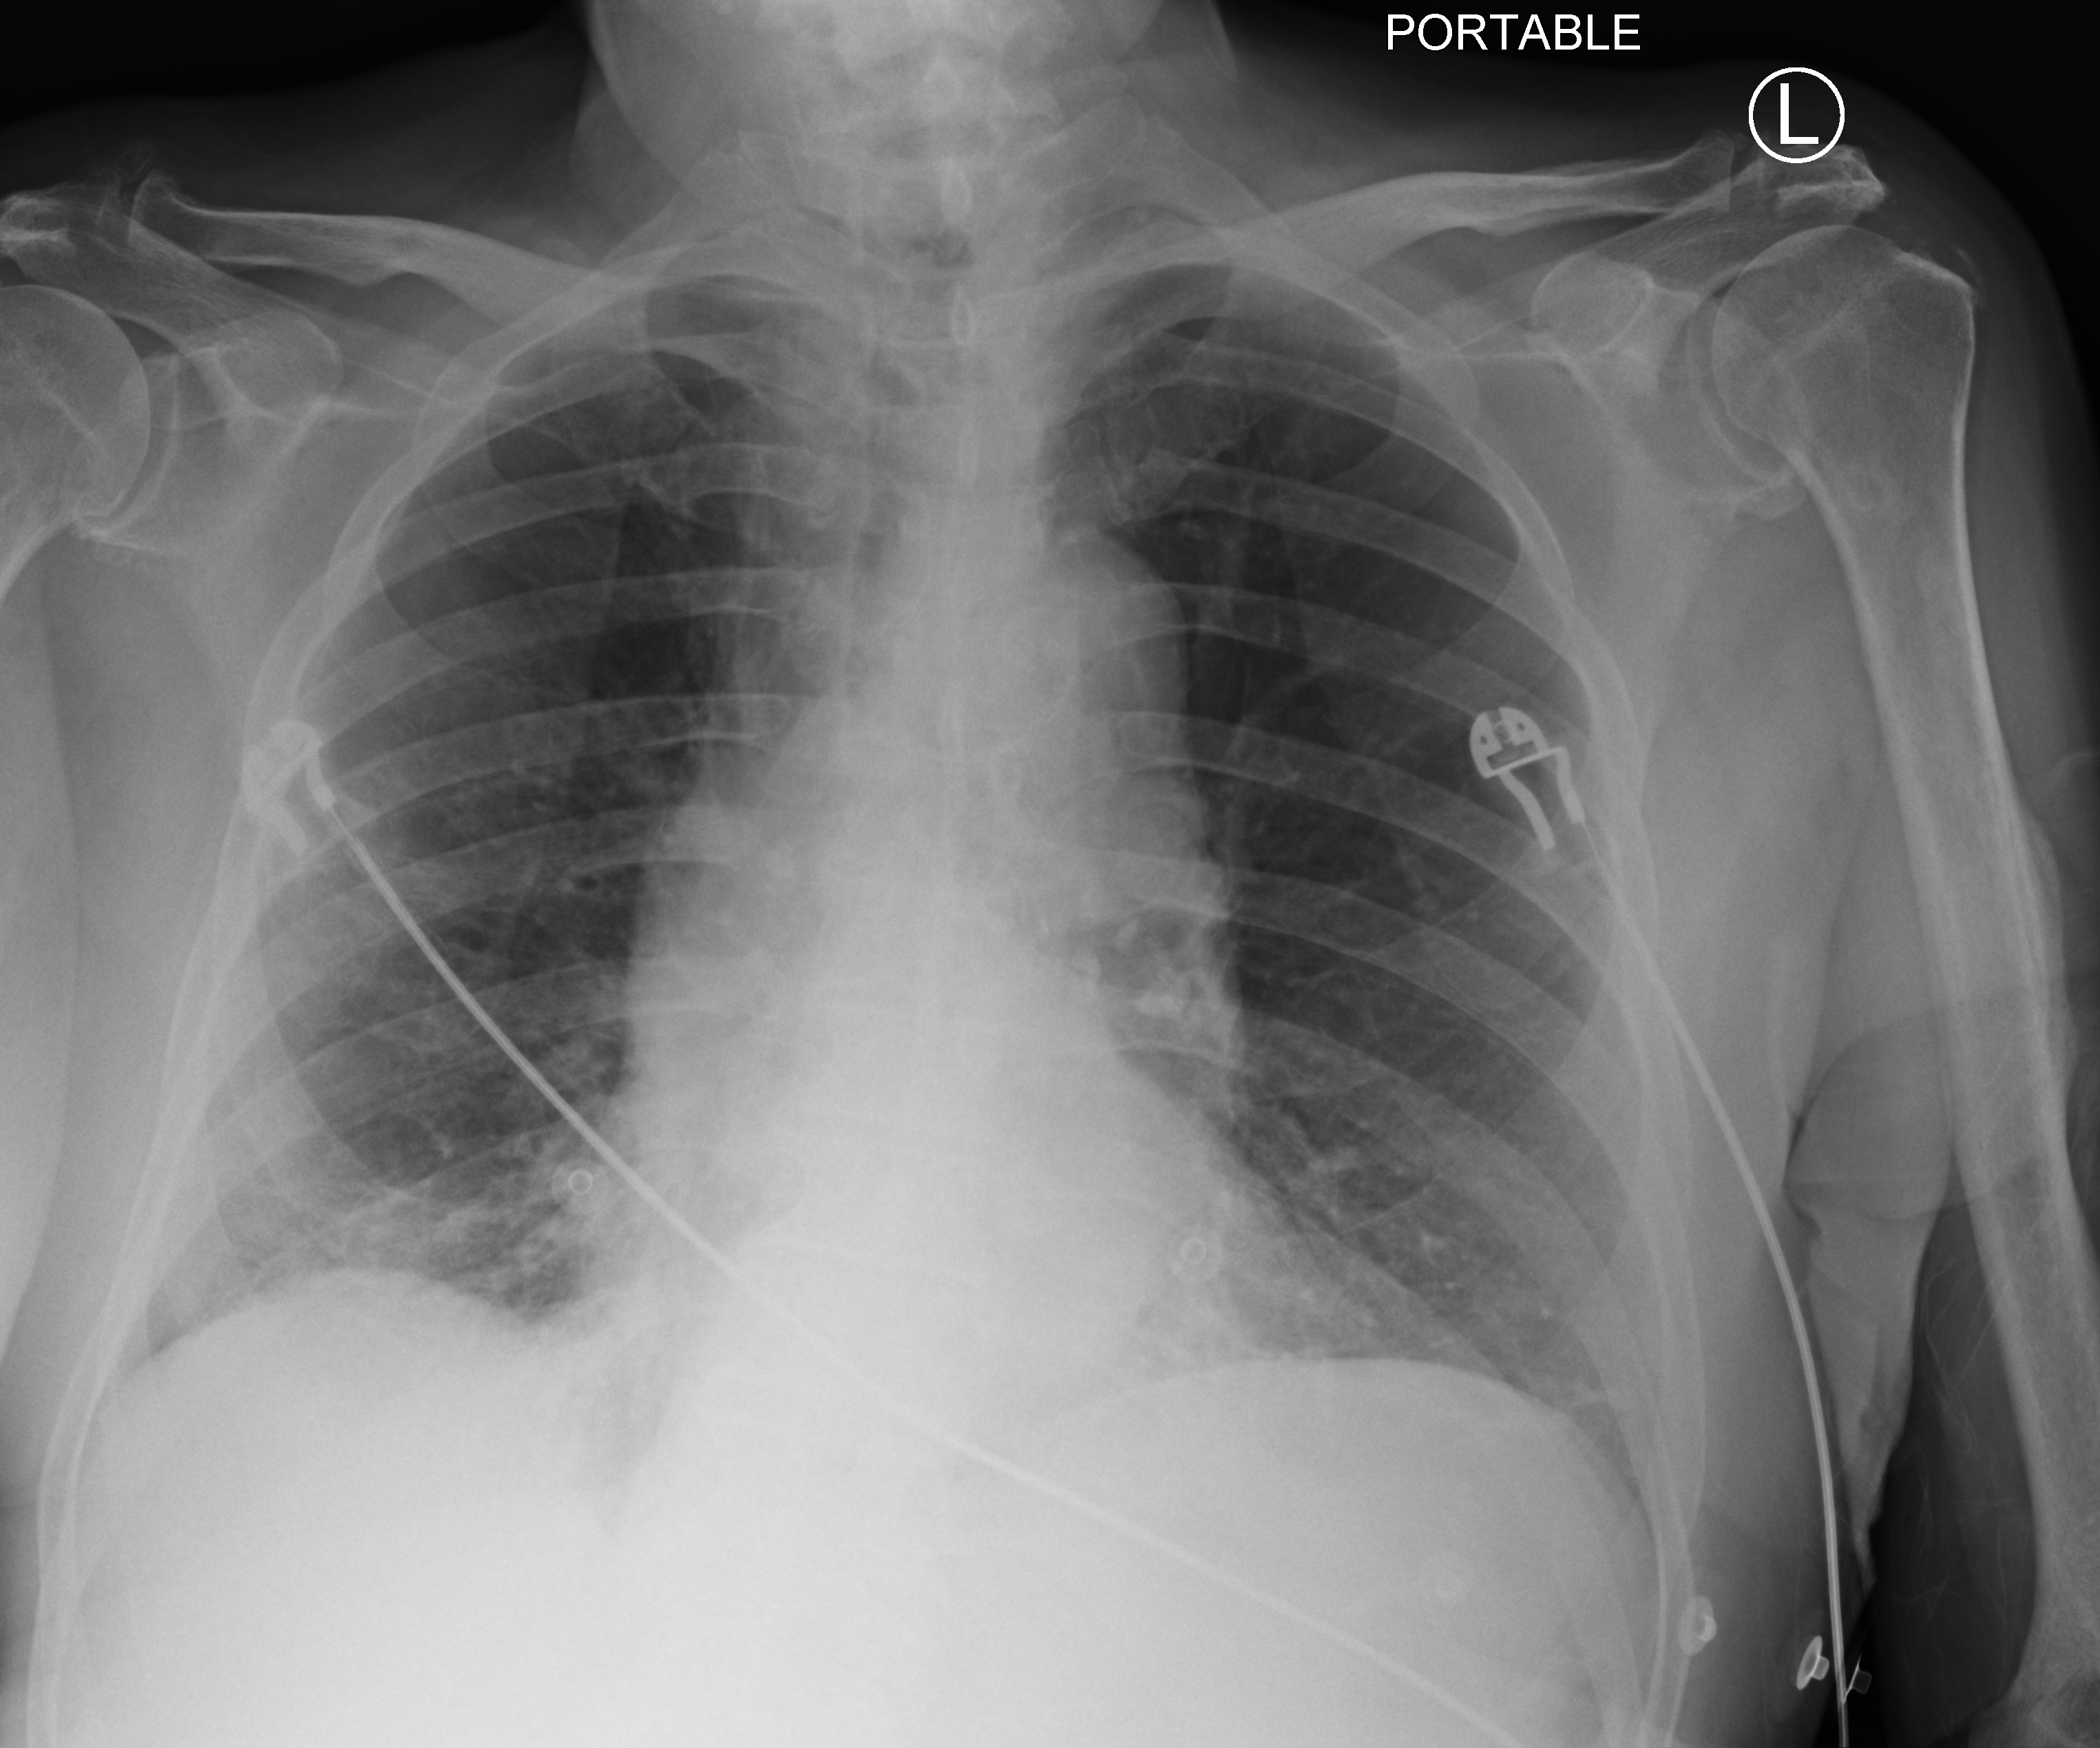
Chest X-ray (portable), anteroposterior (AP) projection. Male patient hospitalised with COVID-19, age 75–90 years.
From the hospital-stay record, not from the radiograph (when in the stay this image was taken is not recorded): mechanically ventilated during this hospital stay: no; admitted to intensive care during this hospital stay: no.